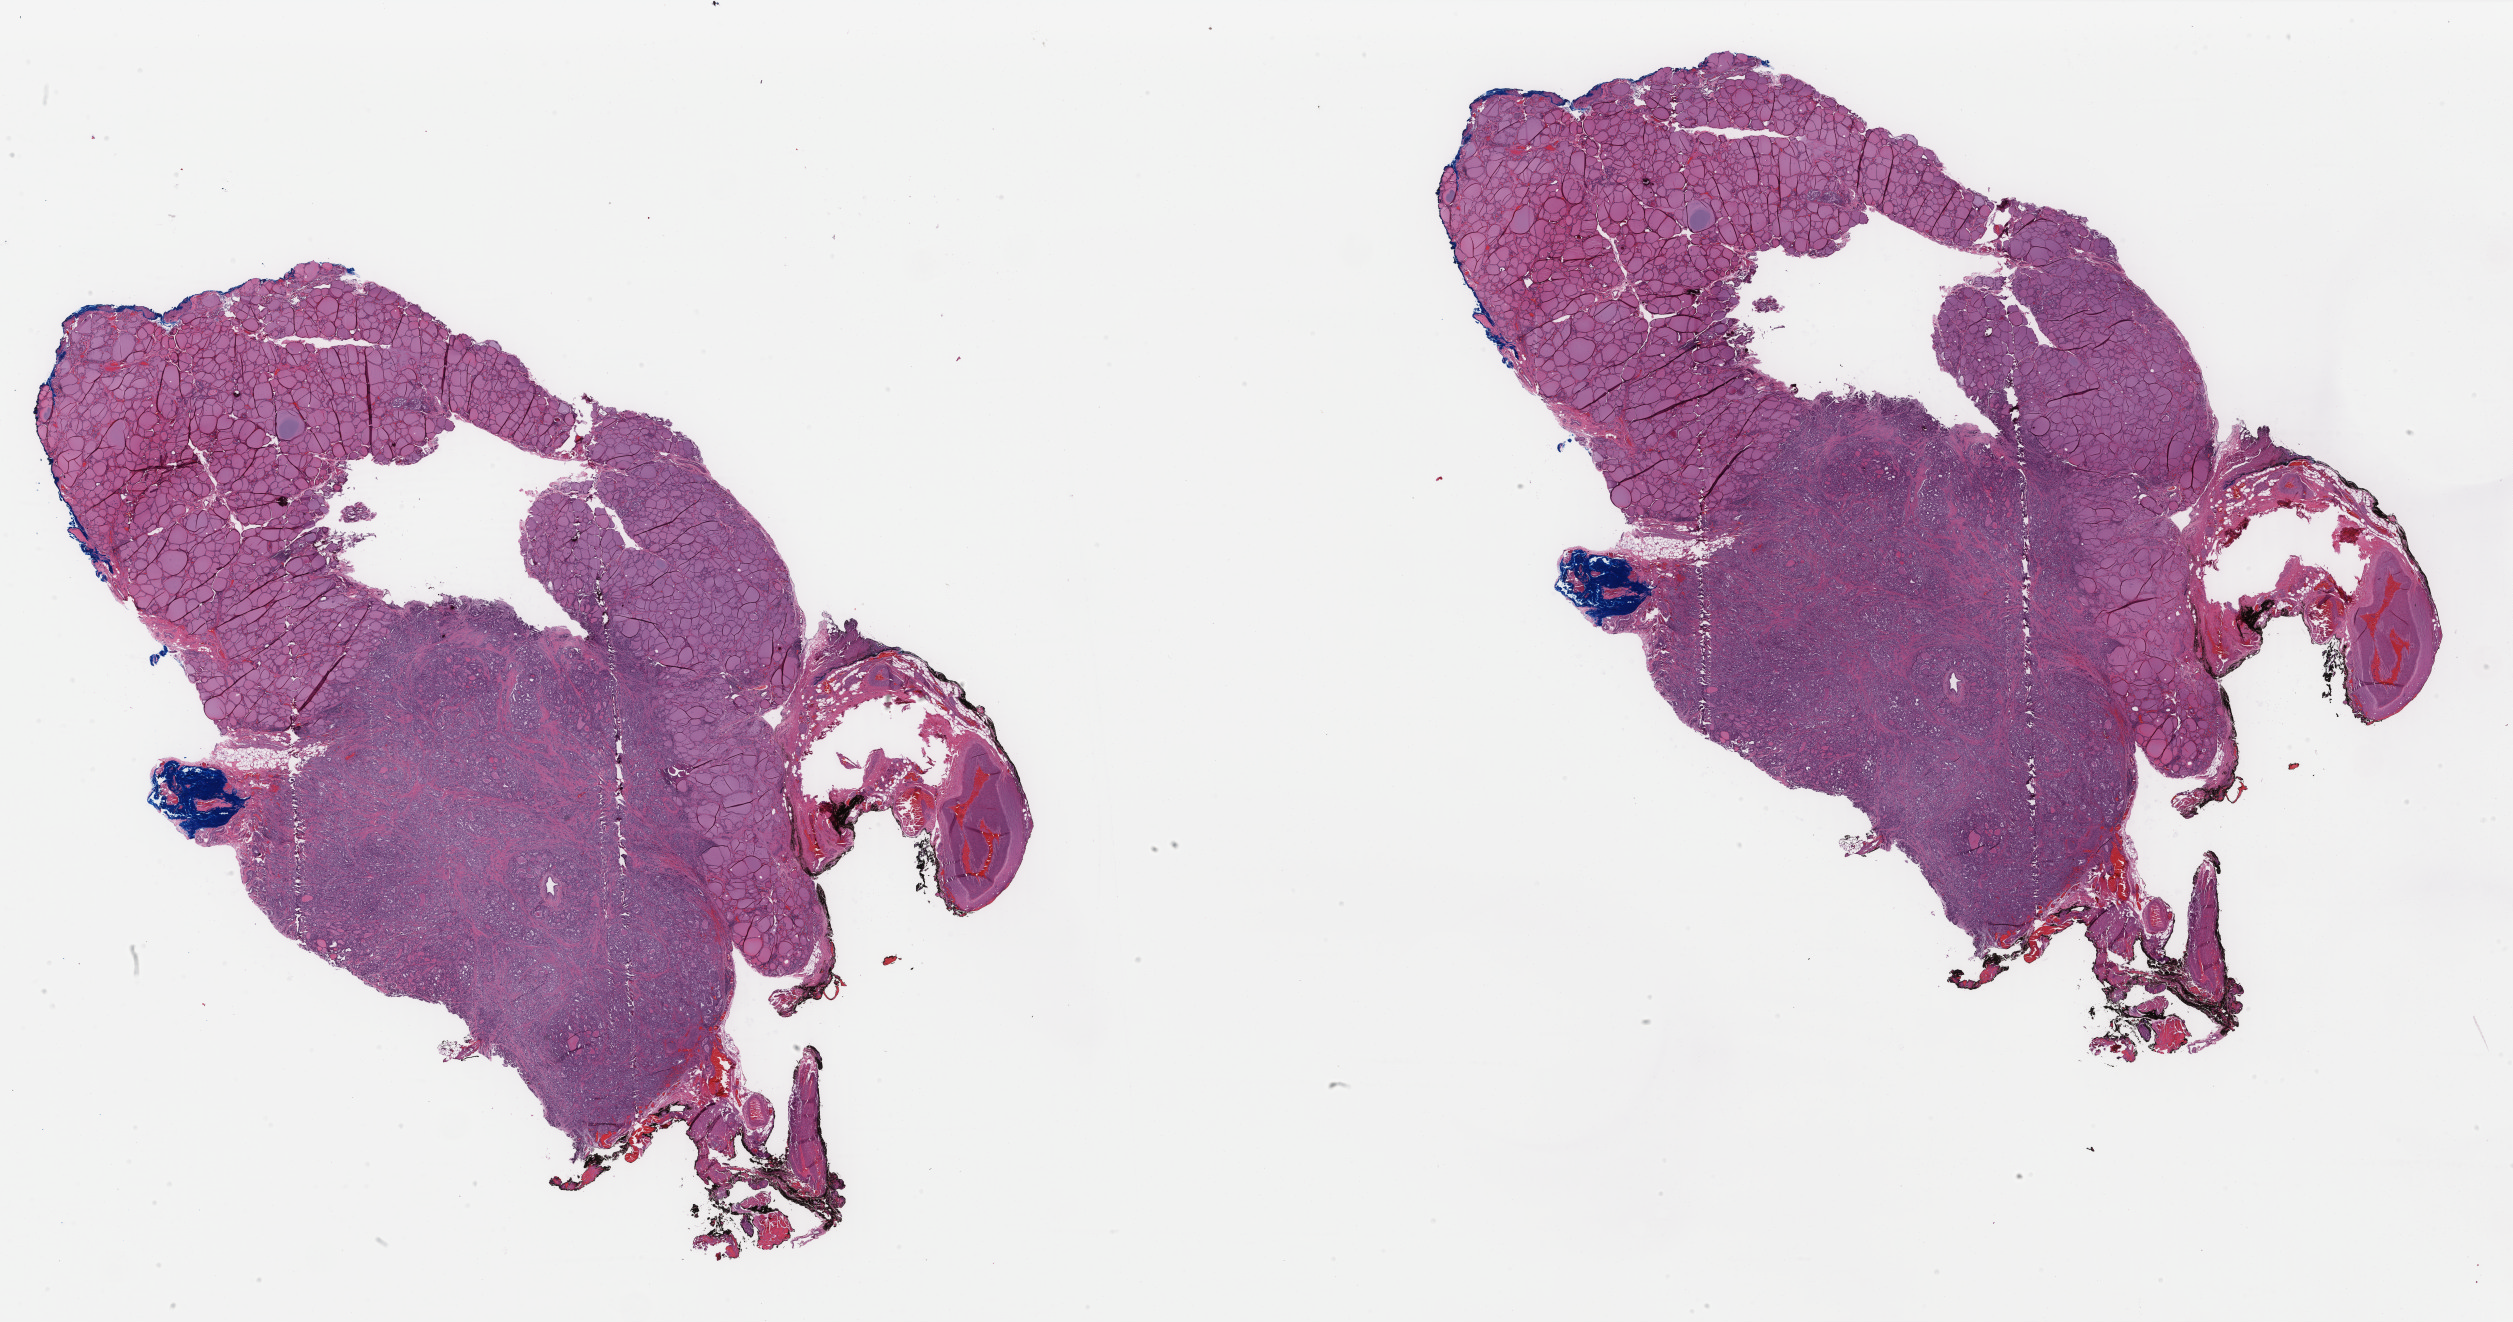
Digitized Hematoxylin and eosin (H&E) stained tissue section (whole slide), a low-resolution overview of the entire scanned area, about 39.9 x 21.0 mm; formalin-fixed paraffin-embedded (FFPE) diagnostic section; primary tumour sample from the thyroid. Female patient; age at initial diagnosis 38 years.
TNM: T1b N1b M0. AJCC pathologic stage: I (7th edition). Histologic diagnosis: Papillary adenocarcinoma, NOS (thyroid gland). Lymph nodes positive (case pathology): 22 of 45 examined.